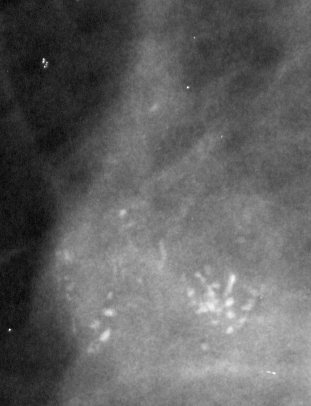
Region of interest cut from a scanned film mammogram (one marked finding), left breast, MLO view.
Finding: calcifications, morphology pleomorphic, distribution clustered; BI-RADS assessment category 4; subtlety rating 5 on a 1 (subtle) to 5 (obvious) scale; pathology (as recorded): malignant.